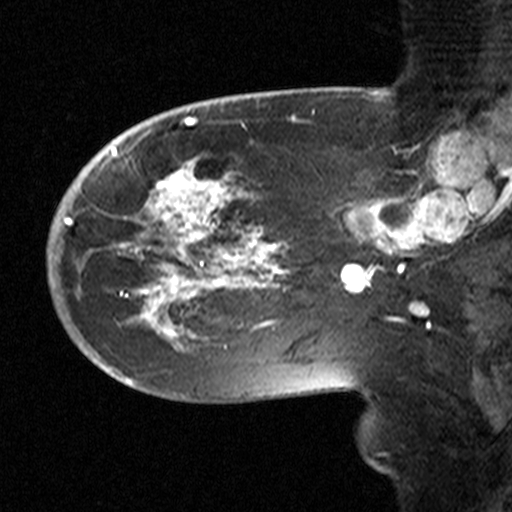
Breast MRI (dynamic contrast-enhanced), one sagittal slice; position 15 of 44 along the scan axis; dynamic contrast-enhanced study with each time point stored as its own series, time point 2 of 3 at this slice position (early post-contrast, ordered by acquisition time); 1.5 T; TE 4.5 ms, TR 11 ms; 512 × 512 image matrix, field of view 200 × 200 mm. Female patient, age 53 years. From the clinical record (not read from this slice): setting: breast cancer imaged before/during neoadjuvant chemotherapy; receptor status: HR-positive, HER2-negative.
Annotated regions visible in this slice (semi-automatic segmentation, software-assisted and operator-edited):
- analysis volume of interest (the breast-tissue region the enhancement analysis was run in; not a lesion): box from (x=58, y=154) to (x=311, y=367) px
- tumour enhancement mask (voxels above the 90 % enhancement threshold inside the analysis volume of interest): (x=65, y=160)–(x=290, y=345)